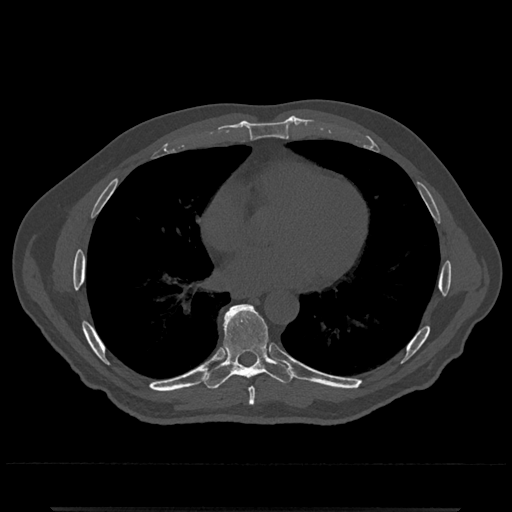
CT including the spine, one axial slice. Slice 679 of 797 in the series (ordered by position). Bone window (W 1800 / L 400 HU). 512 × 512 image matrix, field of view 393 × 393 mm. Patient: male, 67 years. From the clinical record (not read from this slice): primary cancer: prostate.
Outlined on this slice (semi-automatic segmentation, software-assisted and operator-edited):
- T7 vertebra: bounding box (x1, y1, x2, y2) in pixels: (249, 387, 256, 405)
- T8 vertebra: (201, 304, 295, 389)